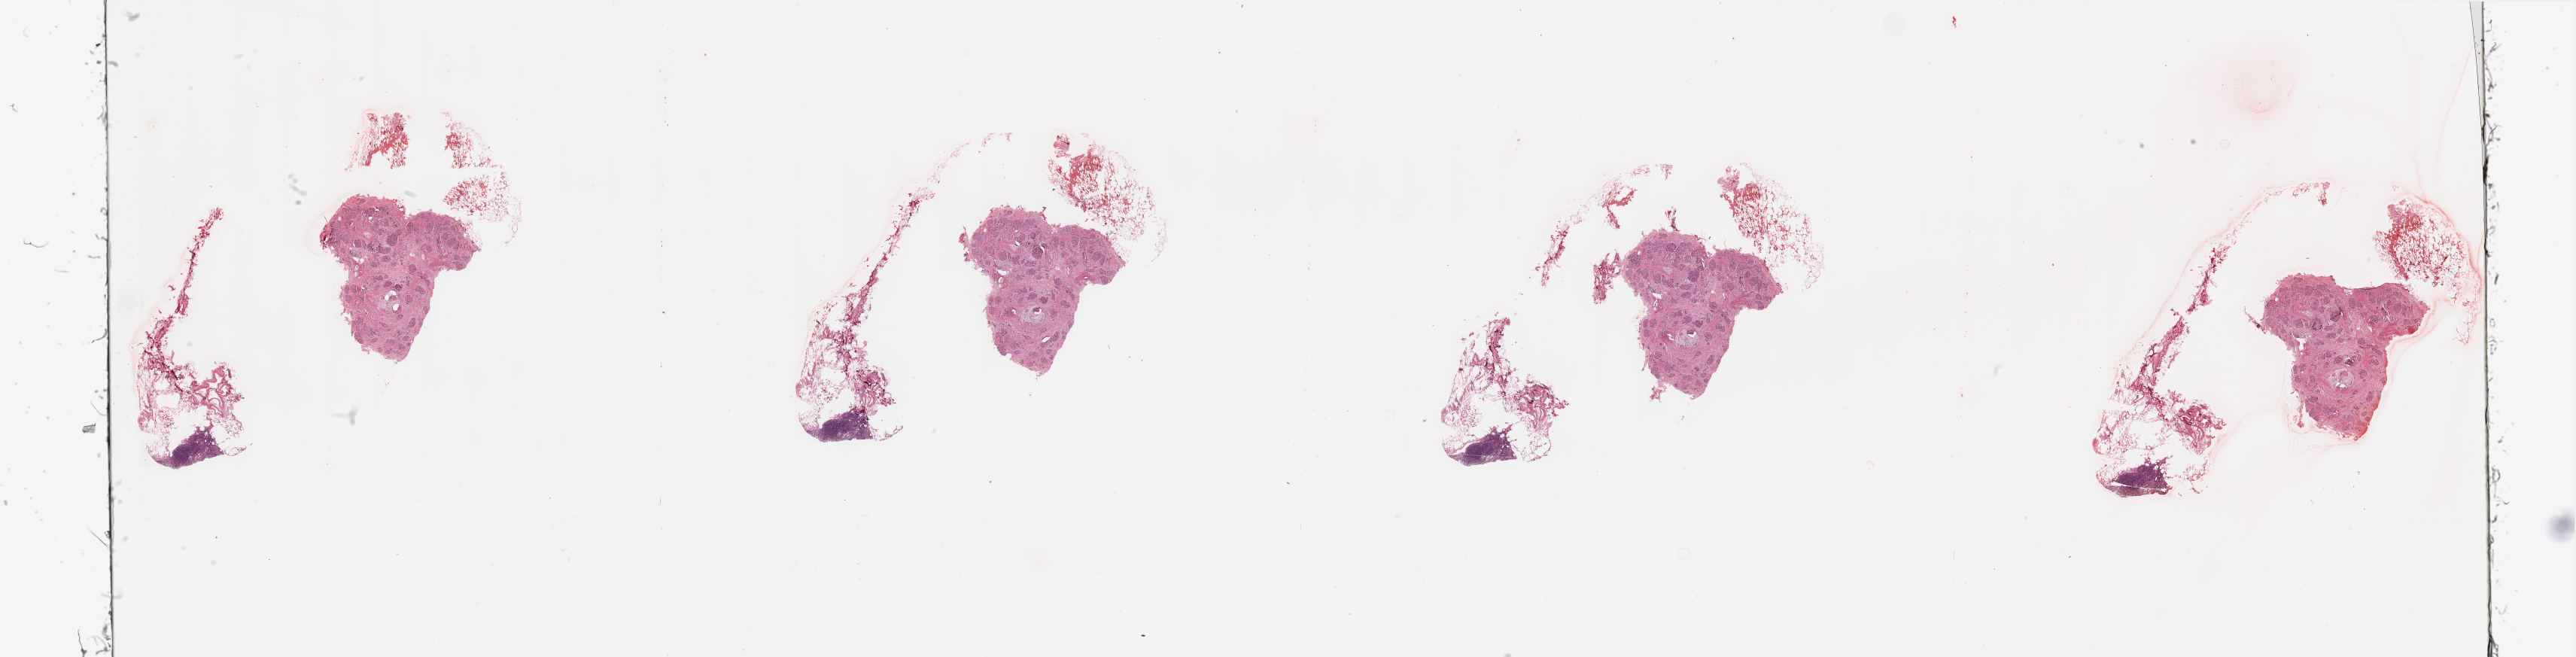
Hematoxylin and eosin (H&E) stained whole-slide image, a low-resolution overview of the entire scanned area, about 54.1 x 13.8 mm (acquisition: 20x scan). Normal (non-tumour) tissue sample, pancreas. Patient: male, age 72 years.
* this section: normal (non-tumour) tissue from the same patient
* patient diagnosis: Infiltrating duct carcinoma, NOS